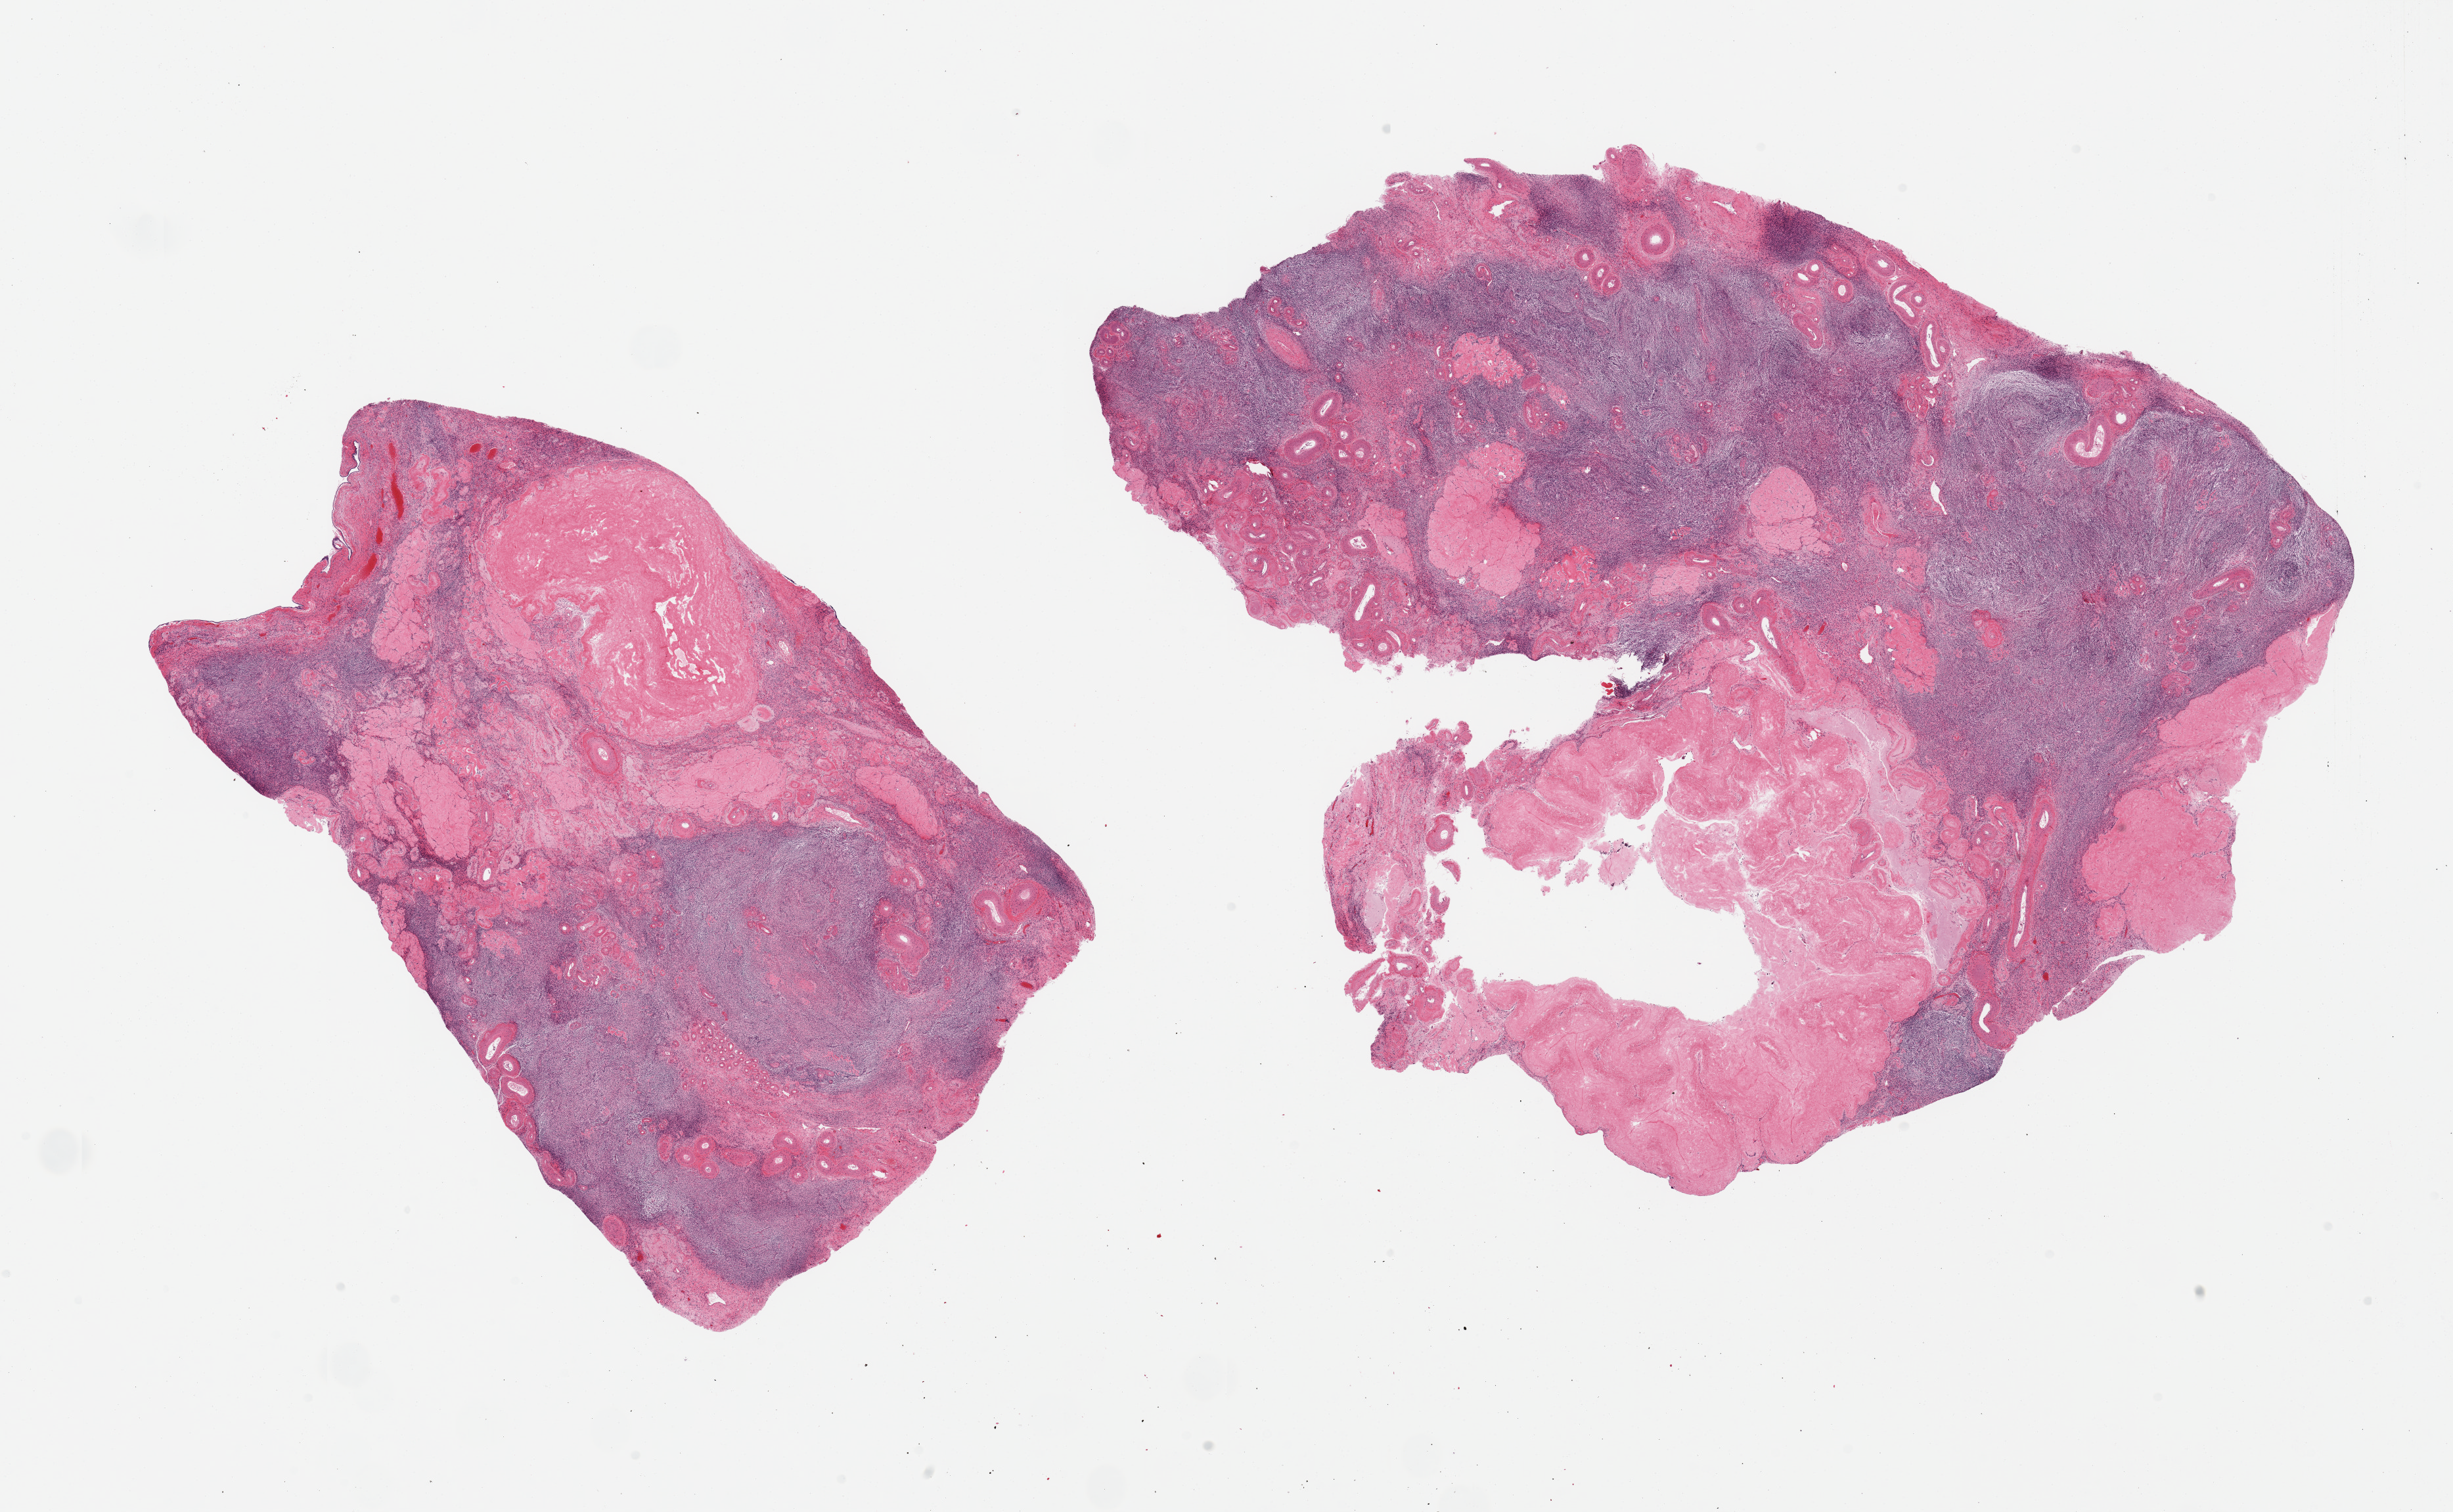
Whole-slide image, H&E stain — shown as a low-resolution overview of the whole scanned area (about 29.5 x 18.2 mm, from a 20x scan). PAXgene-fixed paraffin-embedded (PFPE) section. Section of ovary (target tissue). Tissue donor sample. Donor: female.
• reviewer comment on this tissue sample: 2 pieces; corpora albicantia